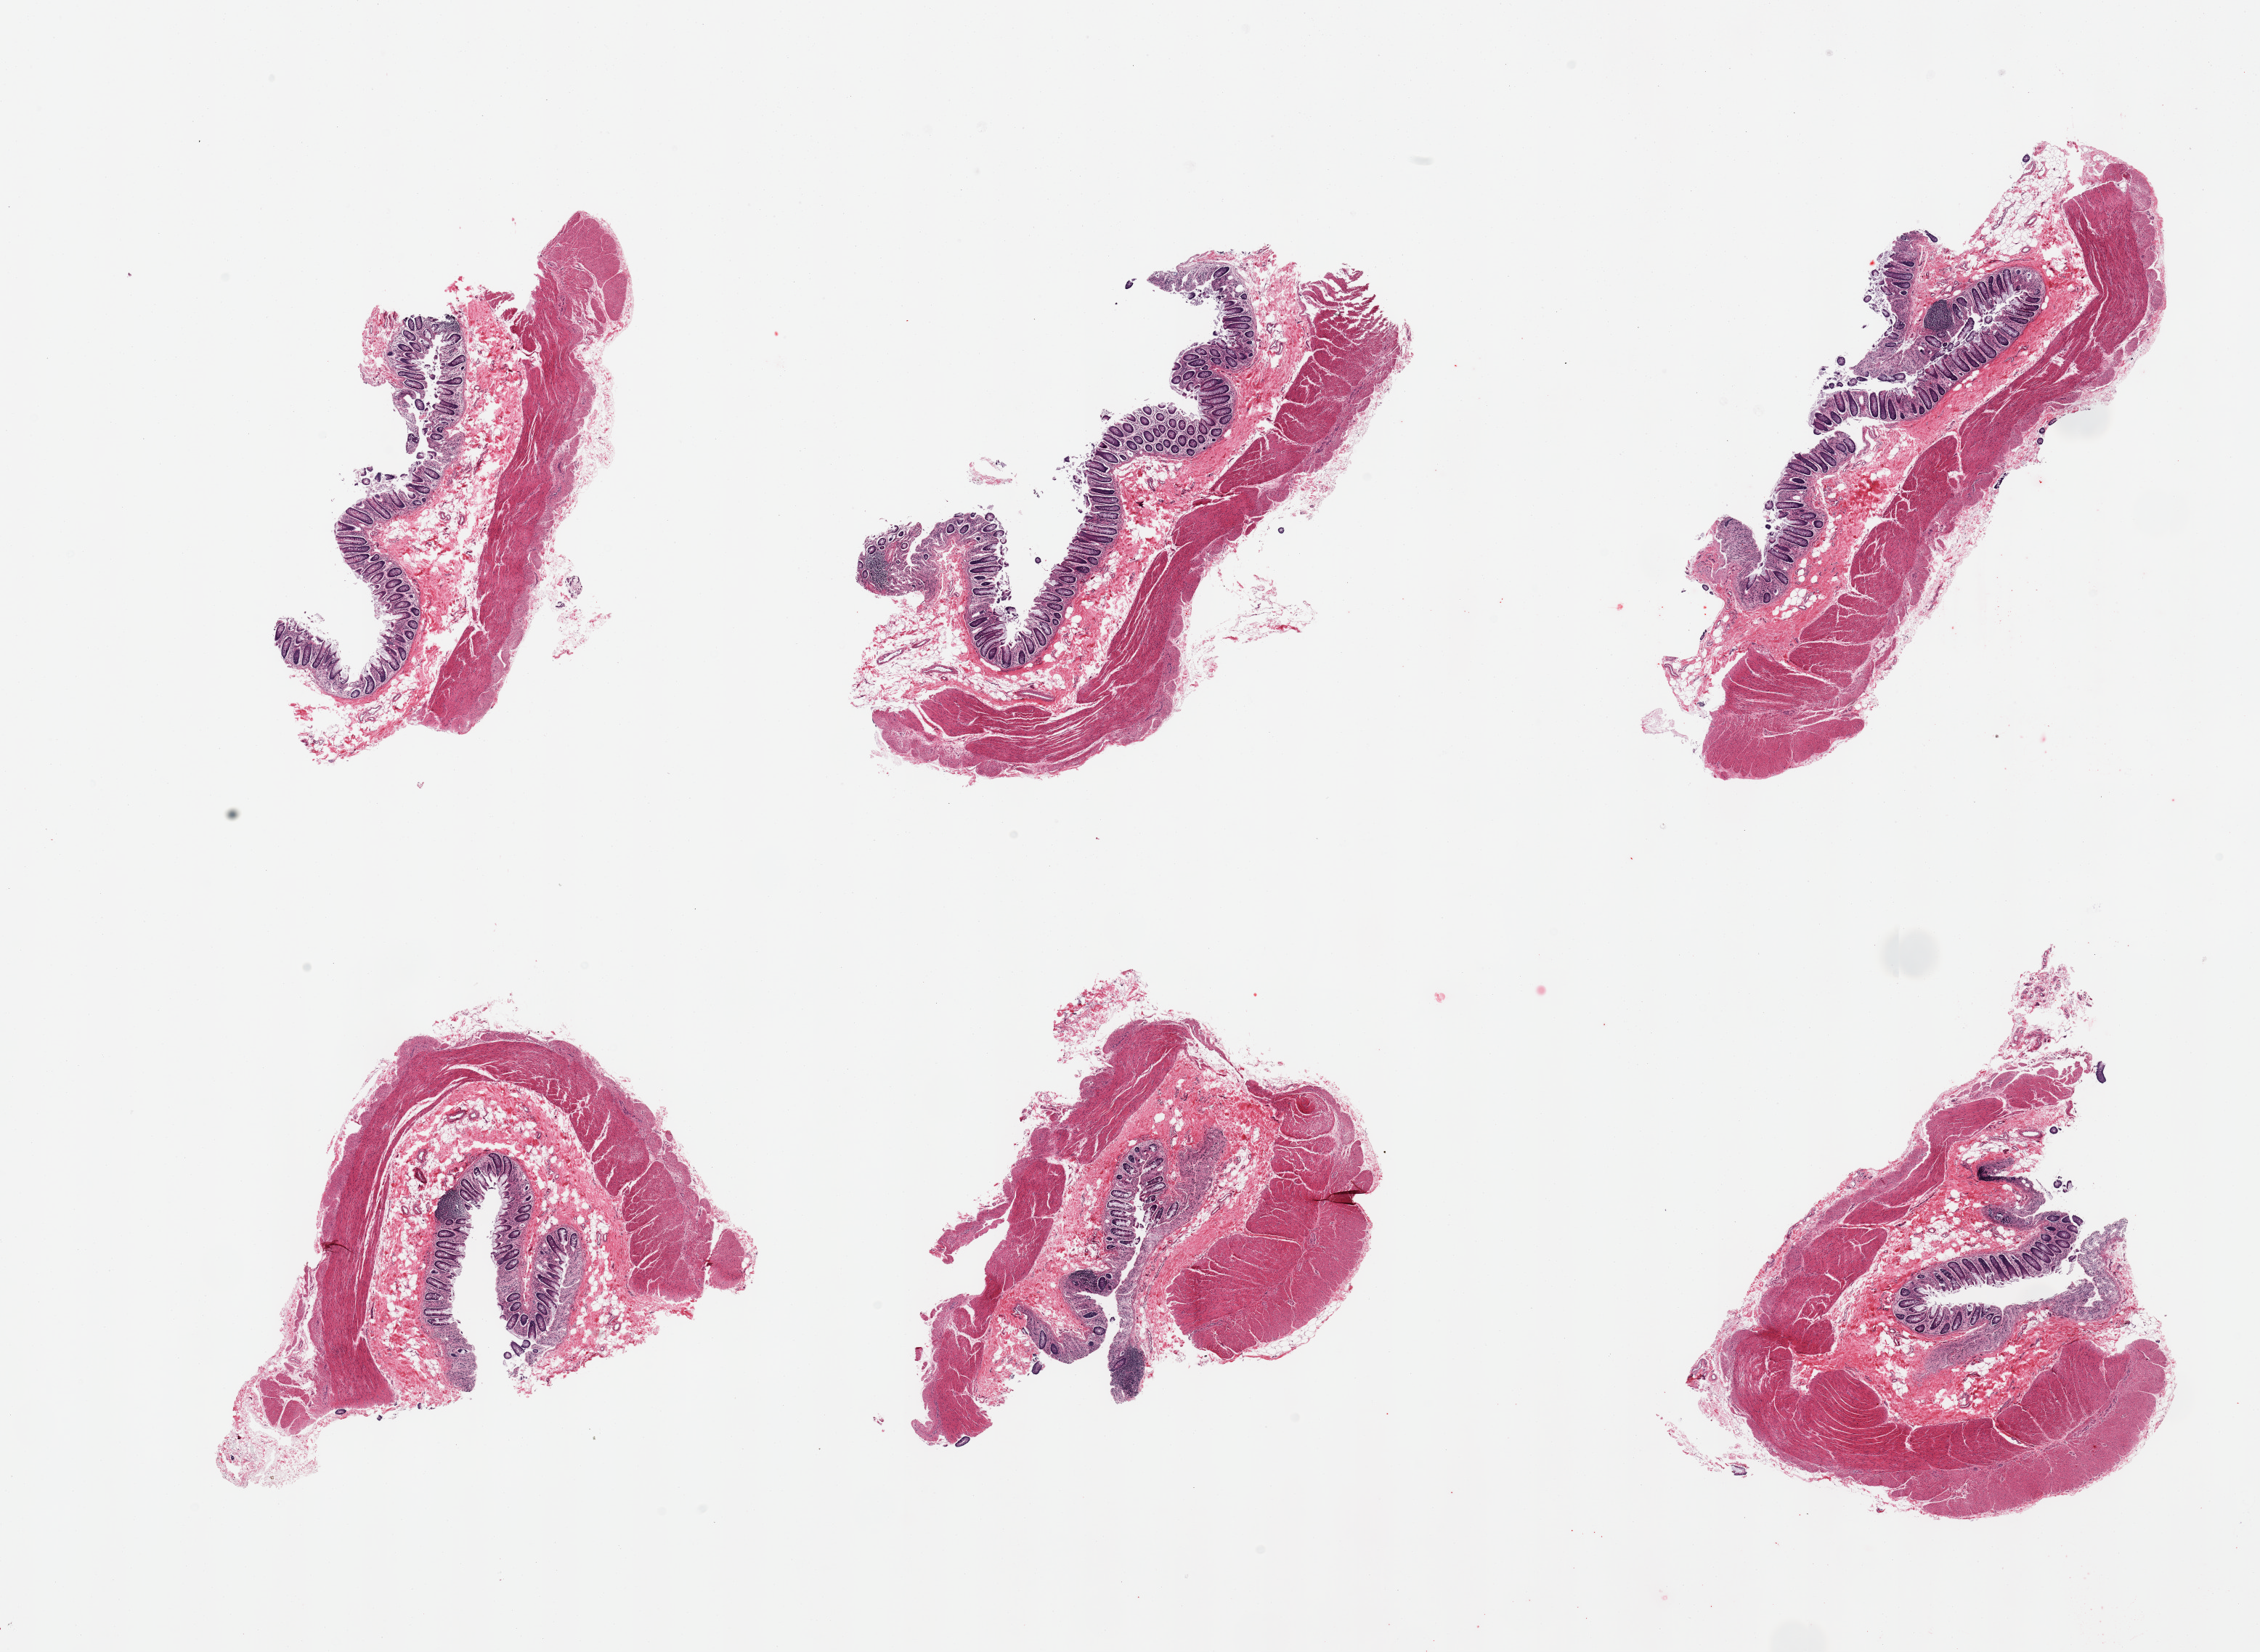
Haematoxylin and eosin whole-slide image, whole scanned area (about 24.6 x 18.0 mm) shown as a low-resolution overview, PAXgene-fixed paraffin-embedded (PFPE) section, section of transverse colon (target tissue), tissue donor sample. Female donor.
* review note (as recorded): 6 pieces; moderately autolyzed mucosa and well preserved muscularis